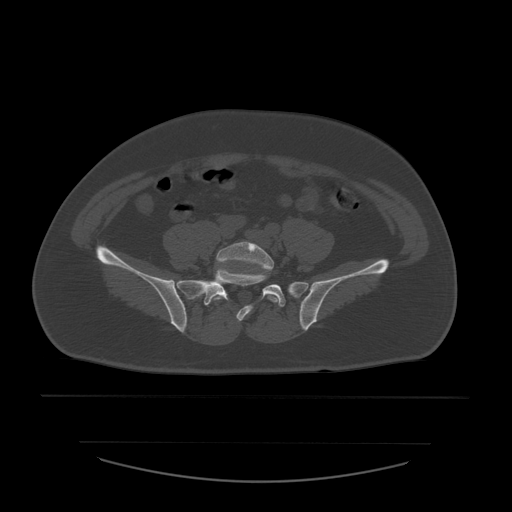
CT including the spine, one axial slice; position 108 of 532 along the scan axis; reconstruction kernel STANDARD; bone window (W 1800 / L 400 HU); 1.25 mm slice thickness; 512 × 512 image matrix. Patient age 44 years. From the clinical record (not read from this slice): primary cancer: soft tissue sarcoma.
Annotated regions visible in this slice (semi-automatic segmentation, software-assisted and operator-edited):
- L5 vertebra: bounding box (x1, y1, x2, y2) in pixels: (212, 242, 281, 322)